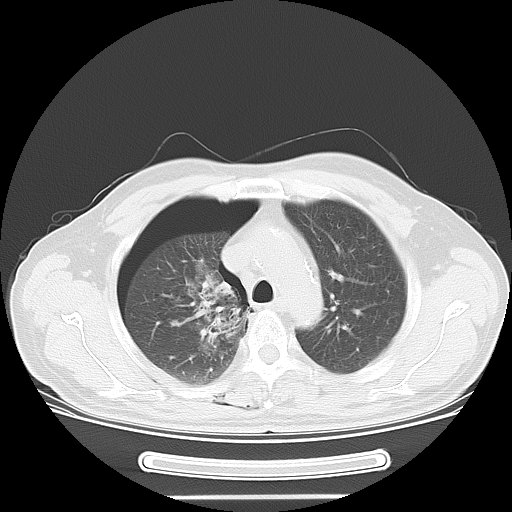
Chest CT, one axial slice. Slice 43 of 57 in the series (ordered by position). Reconstruction kernel LUNG. 120 kVp. Lung window (W 1500 / L -600 HU). 5 mm slice thickness. 512 × 512 image matrix, field of view 376 × 376 mm. Male patient, age 61 years. From the clinical record (not read from this slice): clinical TNM (as recorded): T1c N3 M1b.
Annotated regions visible in this slice (rectangle marked by the reading radiologist):
- lung tumour (recorded histology: adenocarcinoma): bounding box (x1, y1, x2, y2) in pixels: (165, 255, 253, 361)